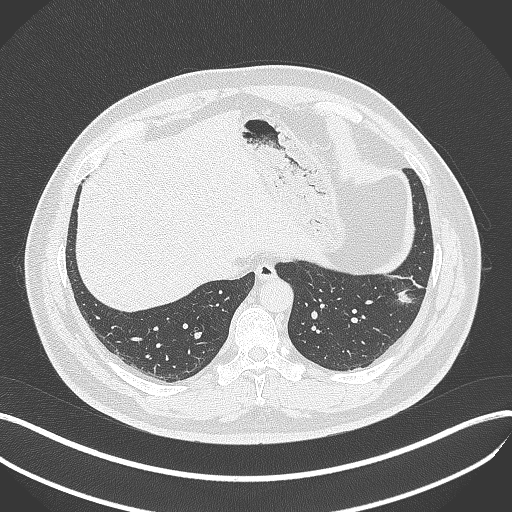
Chest CT, one axial slice; position 107 of 429 along the scan axis; reconstruction kernel B70f; 120 kVp; lung window (W 1500 / L -600 HU); 1 mm slice thickness; 512 × 512 image matrix, field of view 400 × 400 mm. Patient: male, 39 years. From the clinical record (not read from this slice): clinical TNM (as recorded): T2a N0 M0; histopathological grade: G2-3.
Structures marked on this image (rectangle marked by the reading radiologist):
- lung tumour (recorded histology: adenocarcinoma): bounding box (x1, y1, x2, y2) in pixels: (389, 282, 414, 306)